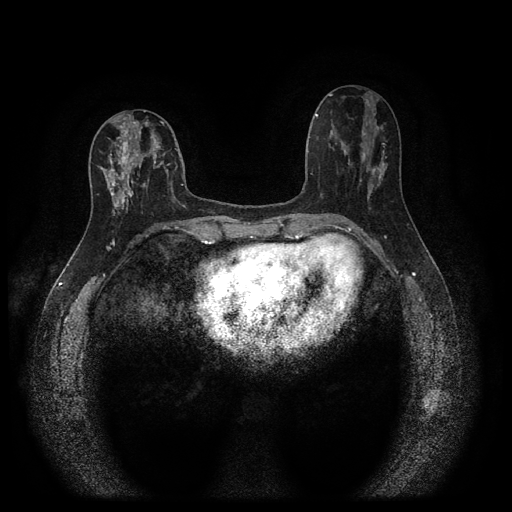
Breast MRI (dynamic contrast-enhanced, multi-phase), one axial slice. Position 44 of 116 along the scan axis. Dynamic contrast-enhanced series, time point 2 of 5 at this slice position (early post-contrast). 1.5 T. TE 2.7 ms, TR 5.4 ms. 2 mm slice thickness. 512 × 512 image matrix, field of view 330 × 330 mm. Patient: female, 47 years.
Outlined on this slice (semi-automatically segmented with operator editing):
- breast lesion (labelled 'tumour' in the annotation; benign lesions carry a separate 'benign' label): bounding box (x1, y1, x2, y2) in pixels: (99, 121, 161, 208)